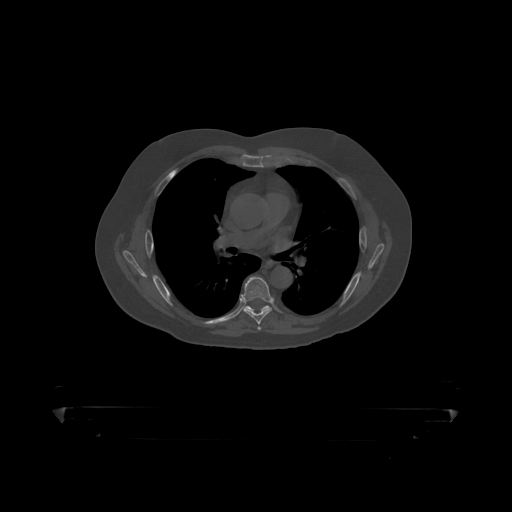
CT including the spine, one axial slice. Position 295 of 390 along the scan axis. 120 kVp. Bone window (W 1800 / L 400 HU). 1.25 mm slice thickness. 512 × 512 image matrix. Patient: male, 60 years. Case-level facts recorded for this patient, not image findings: primary cancer: prostate.
Outlined on this slice (semi-automatically segmented with operator editing):
- T6 vertebra: bounding box (x1, y1, x2, y2) in pixels: (241, 277, 273, 319)
- T7 vertebra: (244, 306, 271, 311)